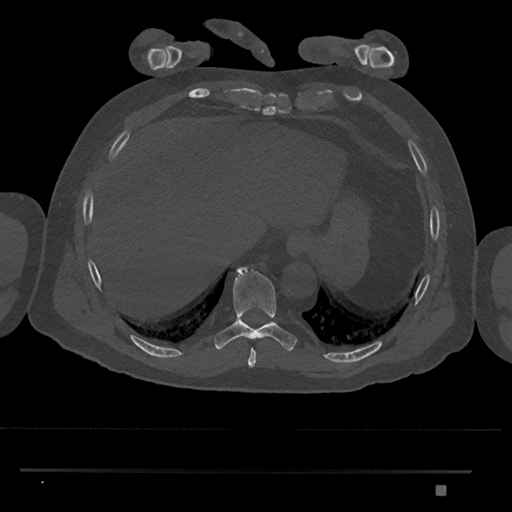
CT including the spine, one axial slice; position 1058 of 1134 along the scan axis; 120 kVp; bone window (W 1800 / L 400 HU); 512 × 512 image matrix. Patient: male, 65 years. From the clinical record (not read from this slice): primary cancer: prostate.
Outlined on this slice (semi-automatically segmented with operator editing):
- T8 vertebra: bounding box [x1, y1, x2, y2] px = [247, 348, 256, 367]
- T9 vertebra: [215, 266, 298, 351]